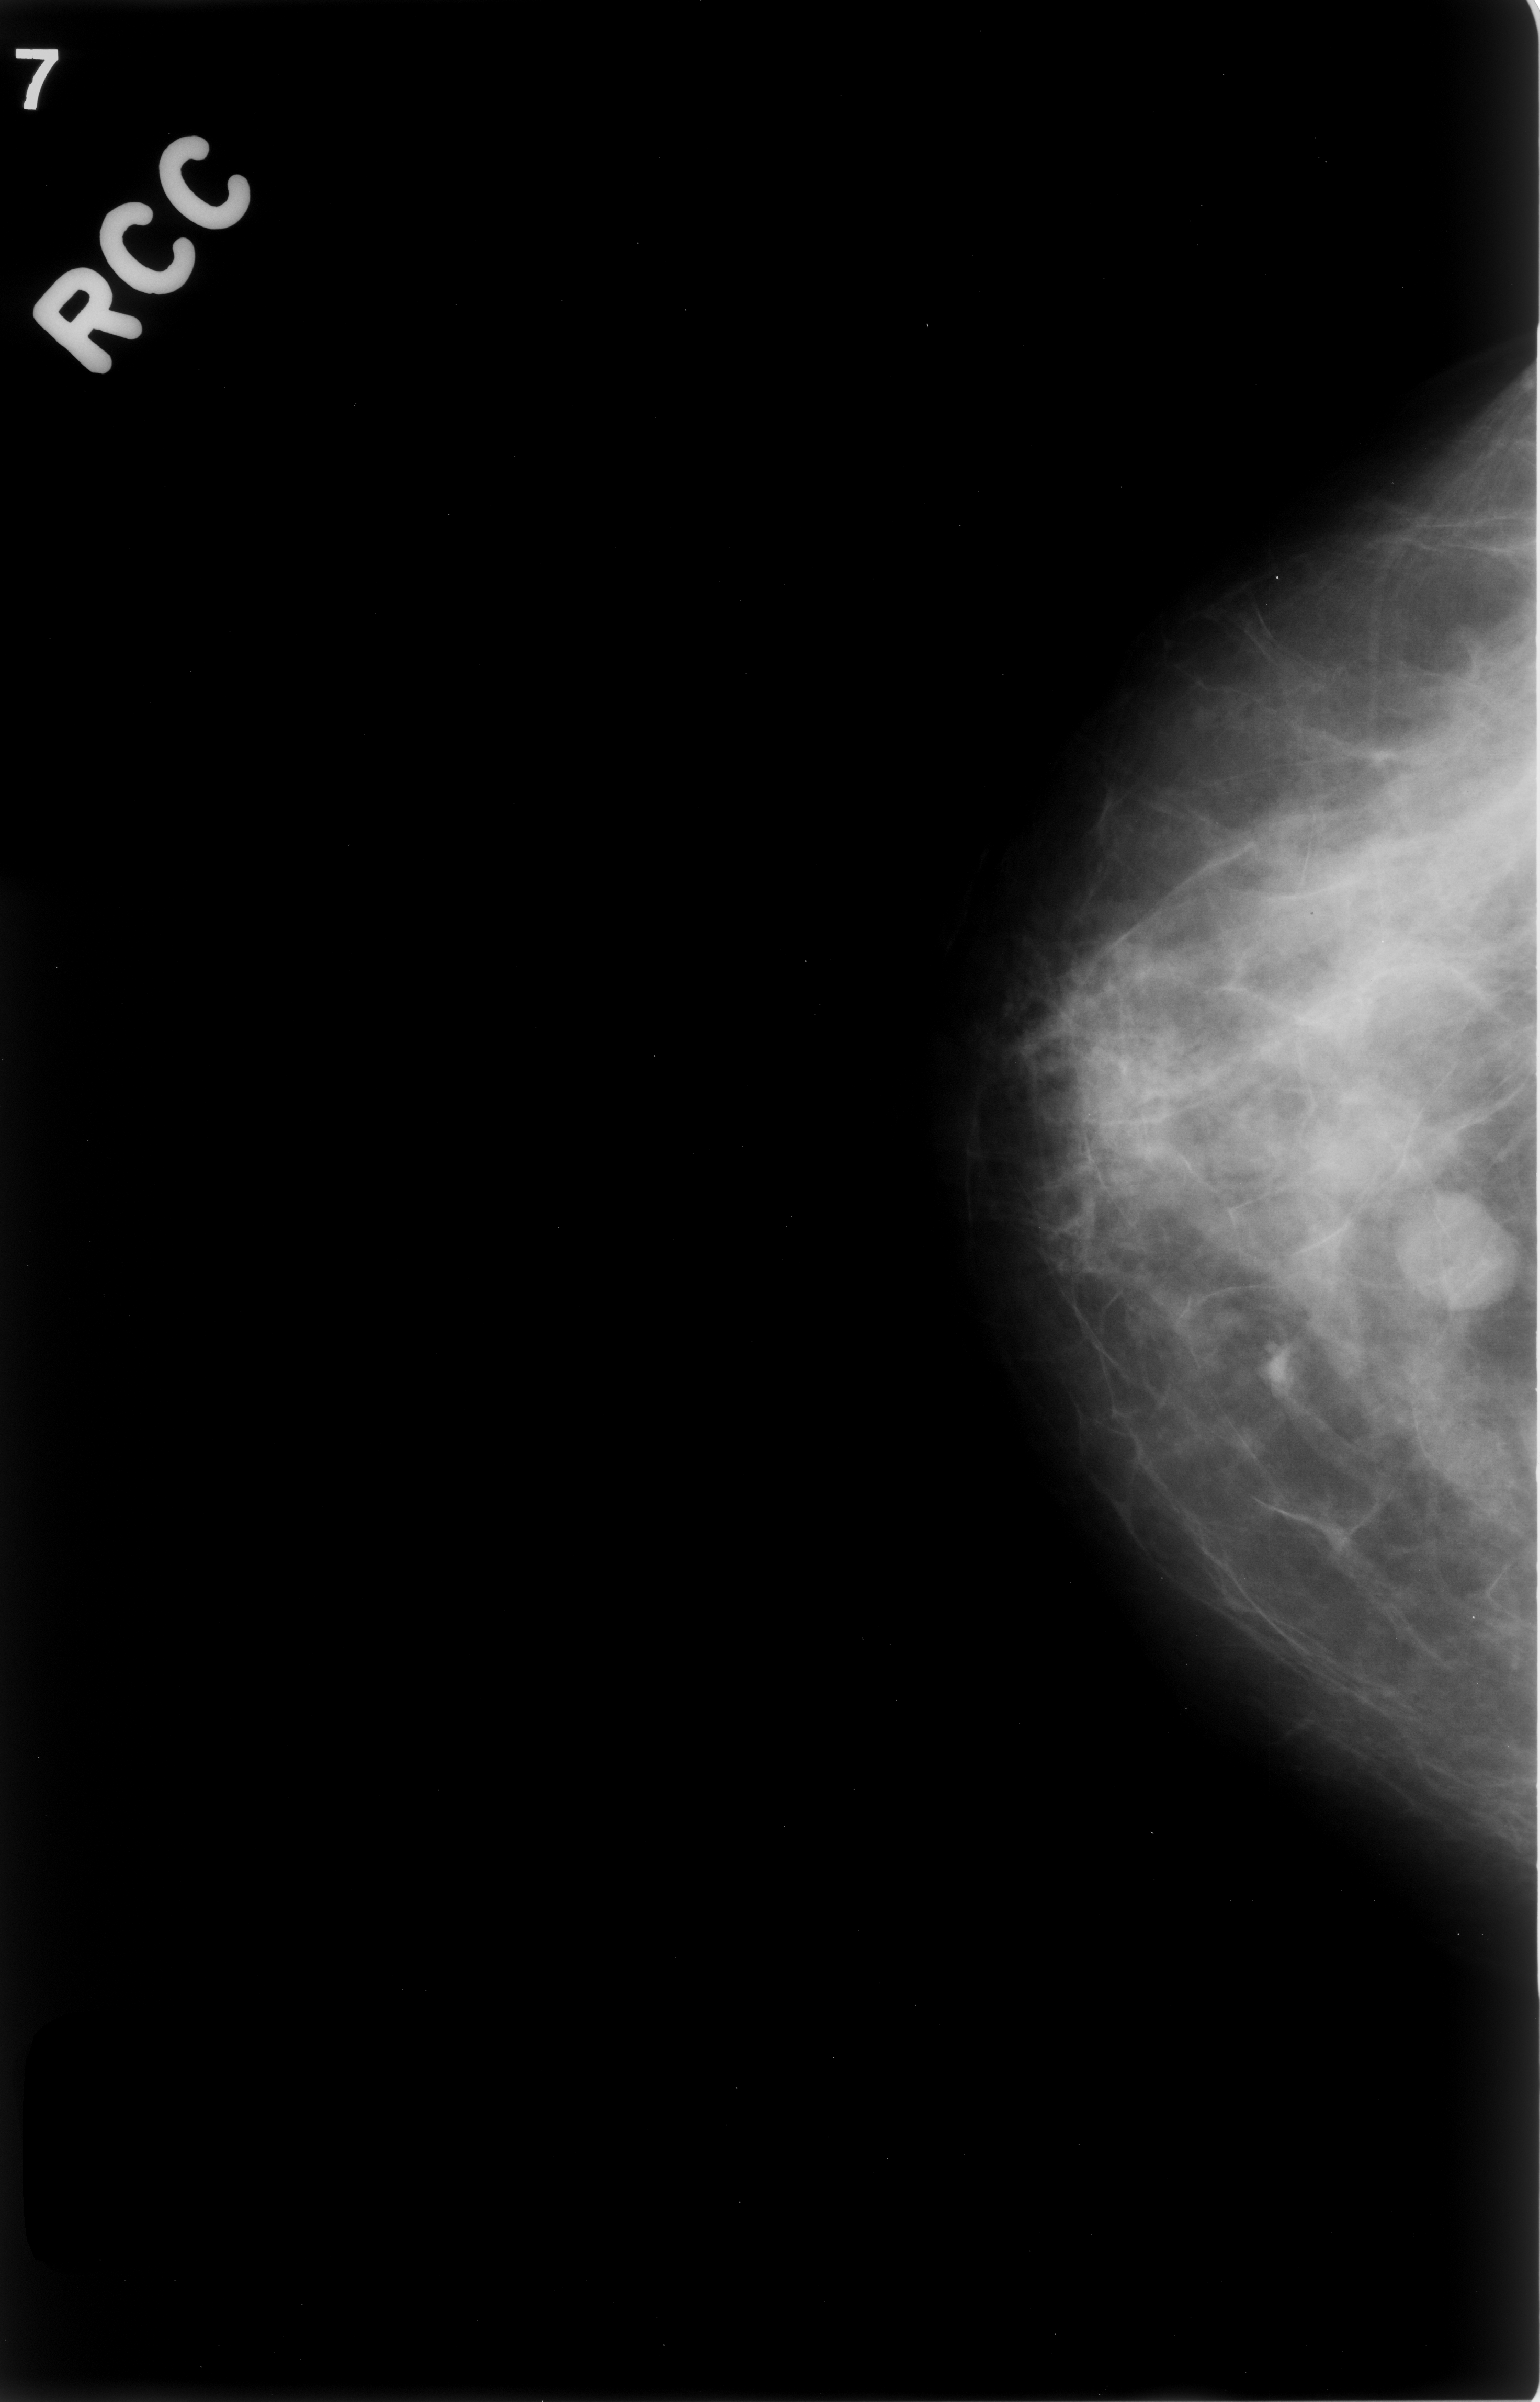
Mammogram (digitized film), right breast, craniocaudal (CC) view.
- Mass, shape oval, margins circumscribed; BI-RADS assessment category 3; subtlety rating 5 on a 1 (subtle) to 5 (obvious) scale; pathology result (as recorded, not read from the image): benign.